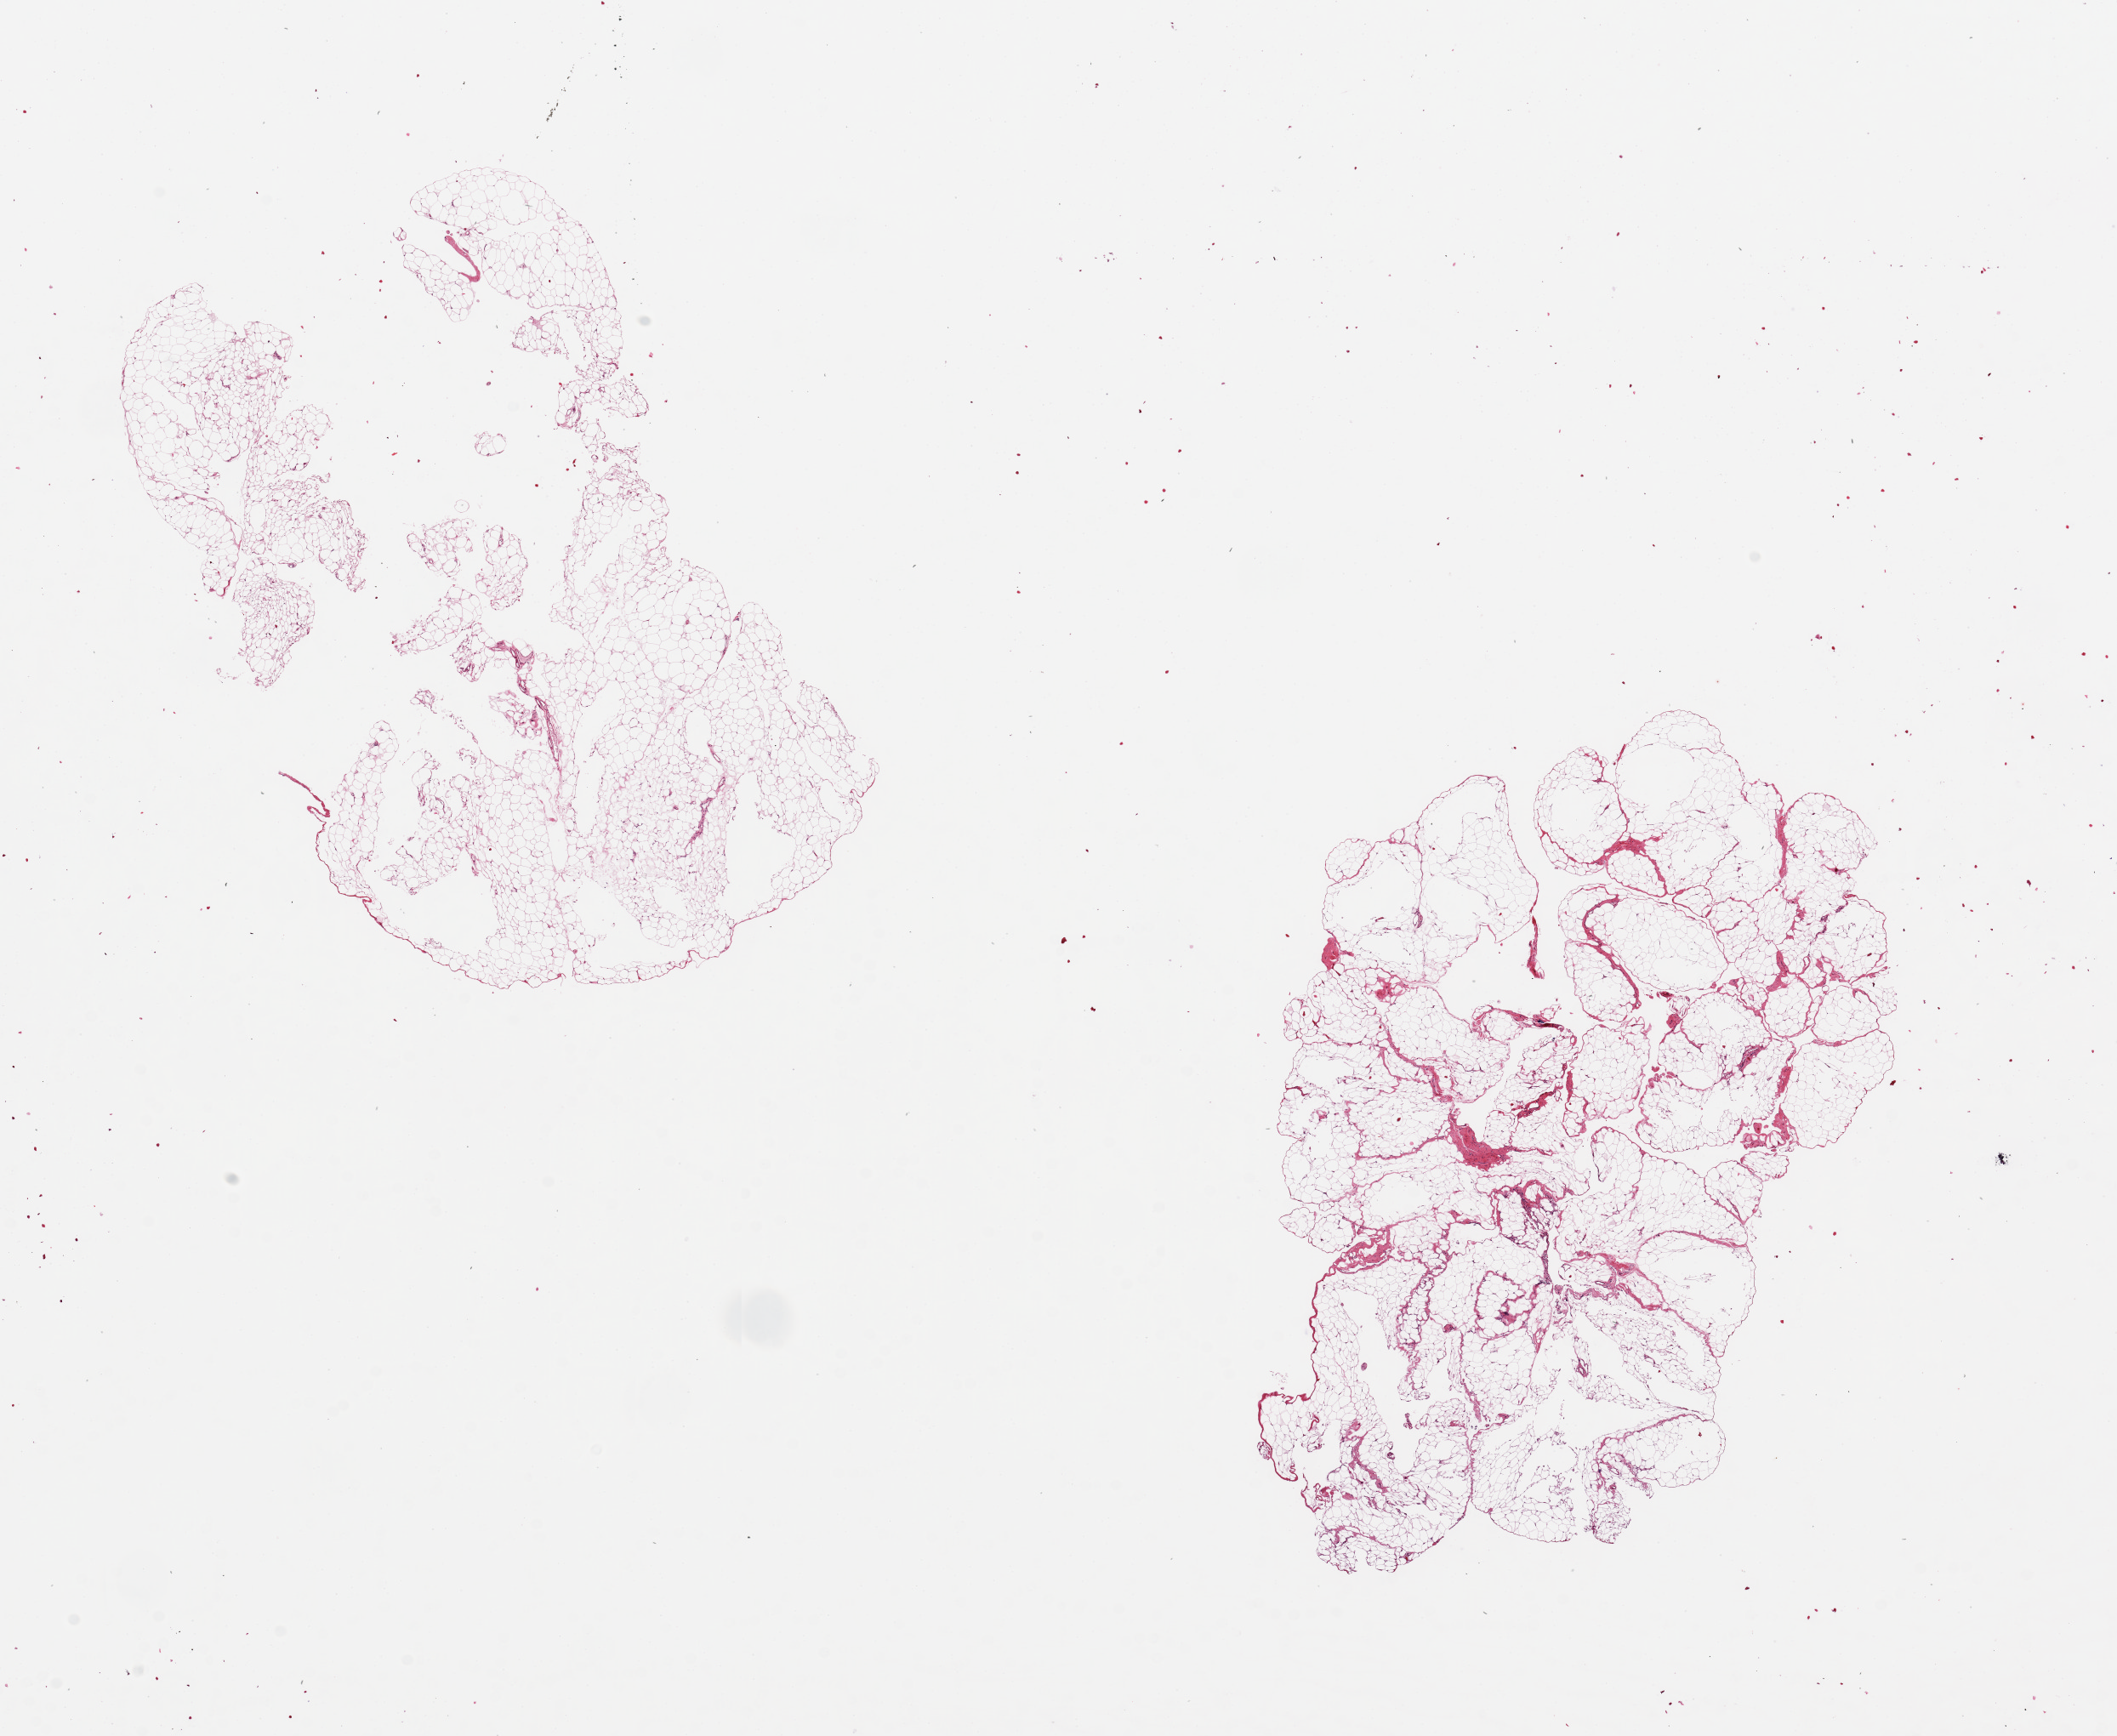
Hematoxylin and eosin (H&E) whole-slide image — shown as a low-resolution overview of the whole scanned area (about 19.7 x 16.1 mm, from a 20x scan). PAXgene-fixed paraffin-embedded (PFPE) section. Section of omentum (target tissue). Donor tissue sample. Donor sex: male.
- review note (as recorded): 2 ~7x5mm pieces